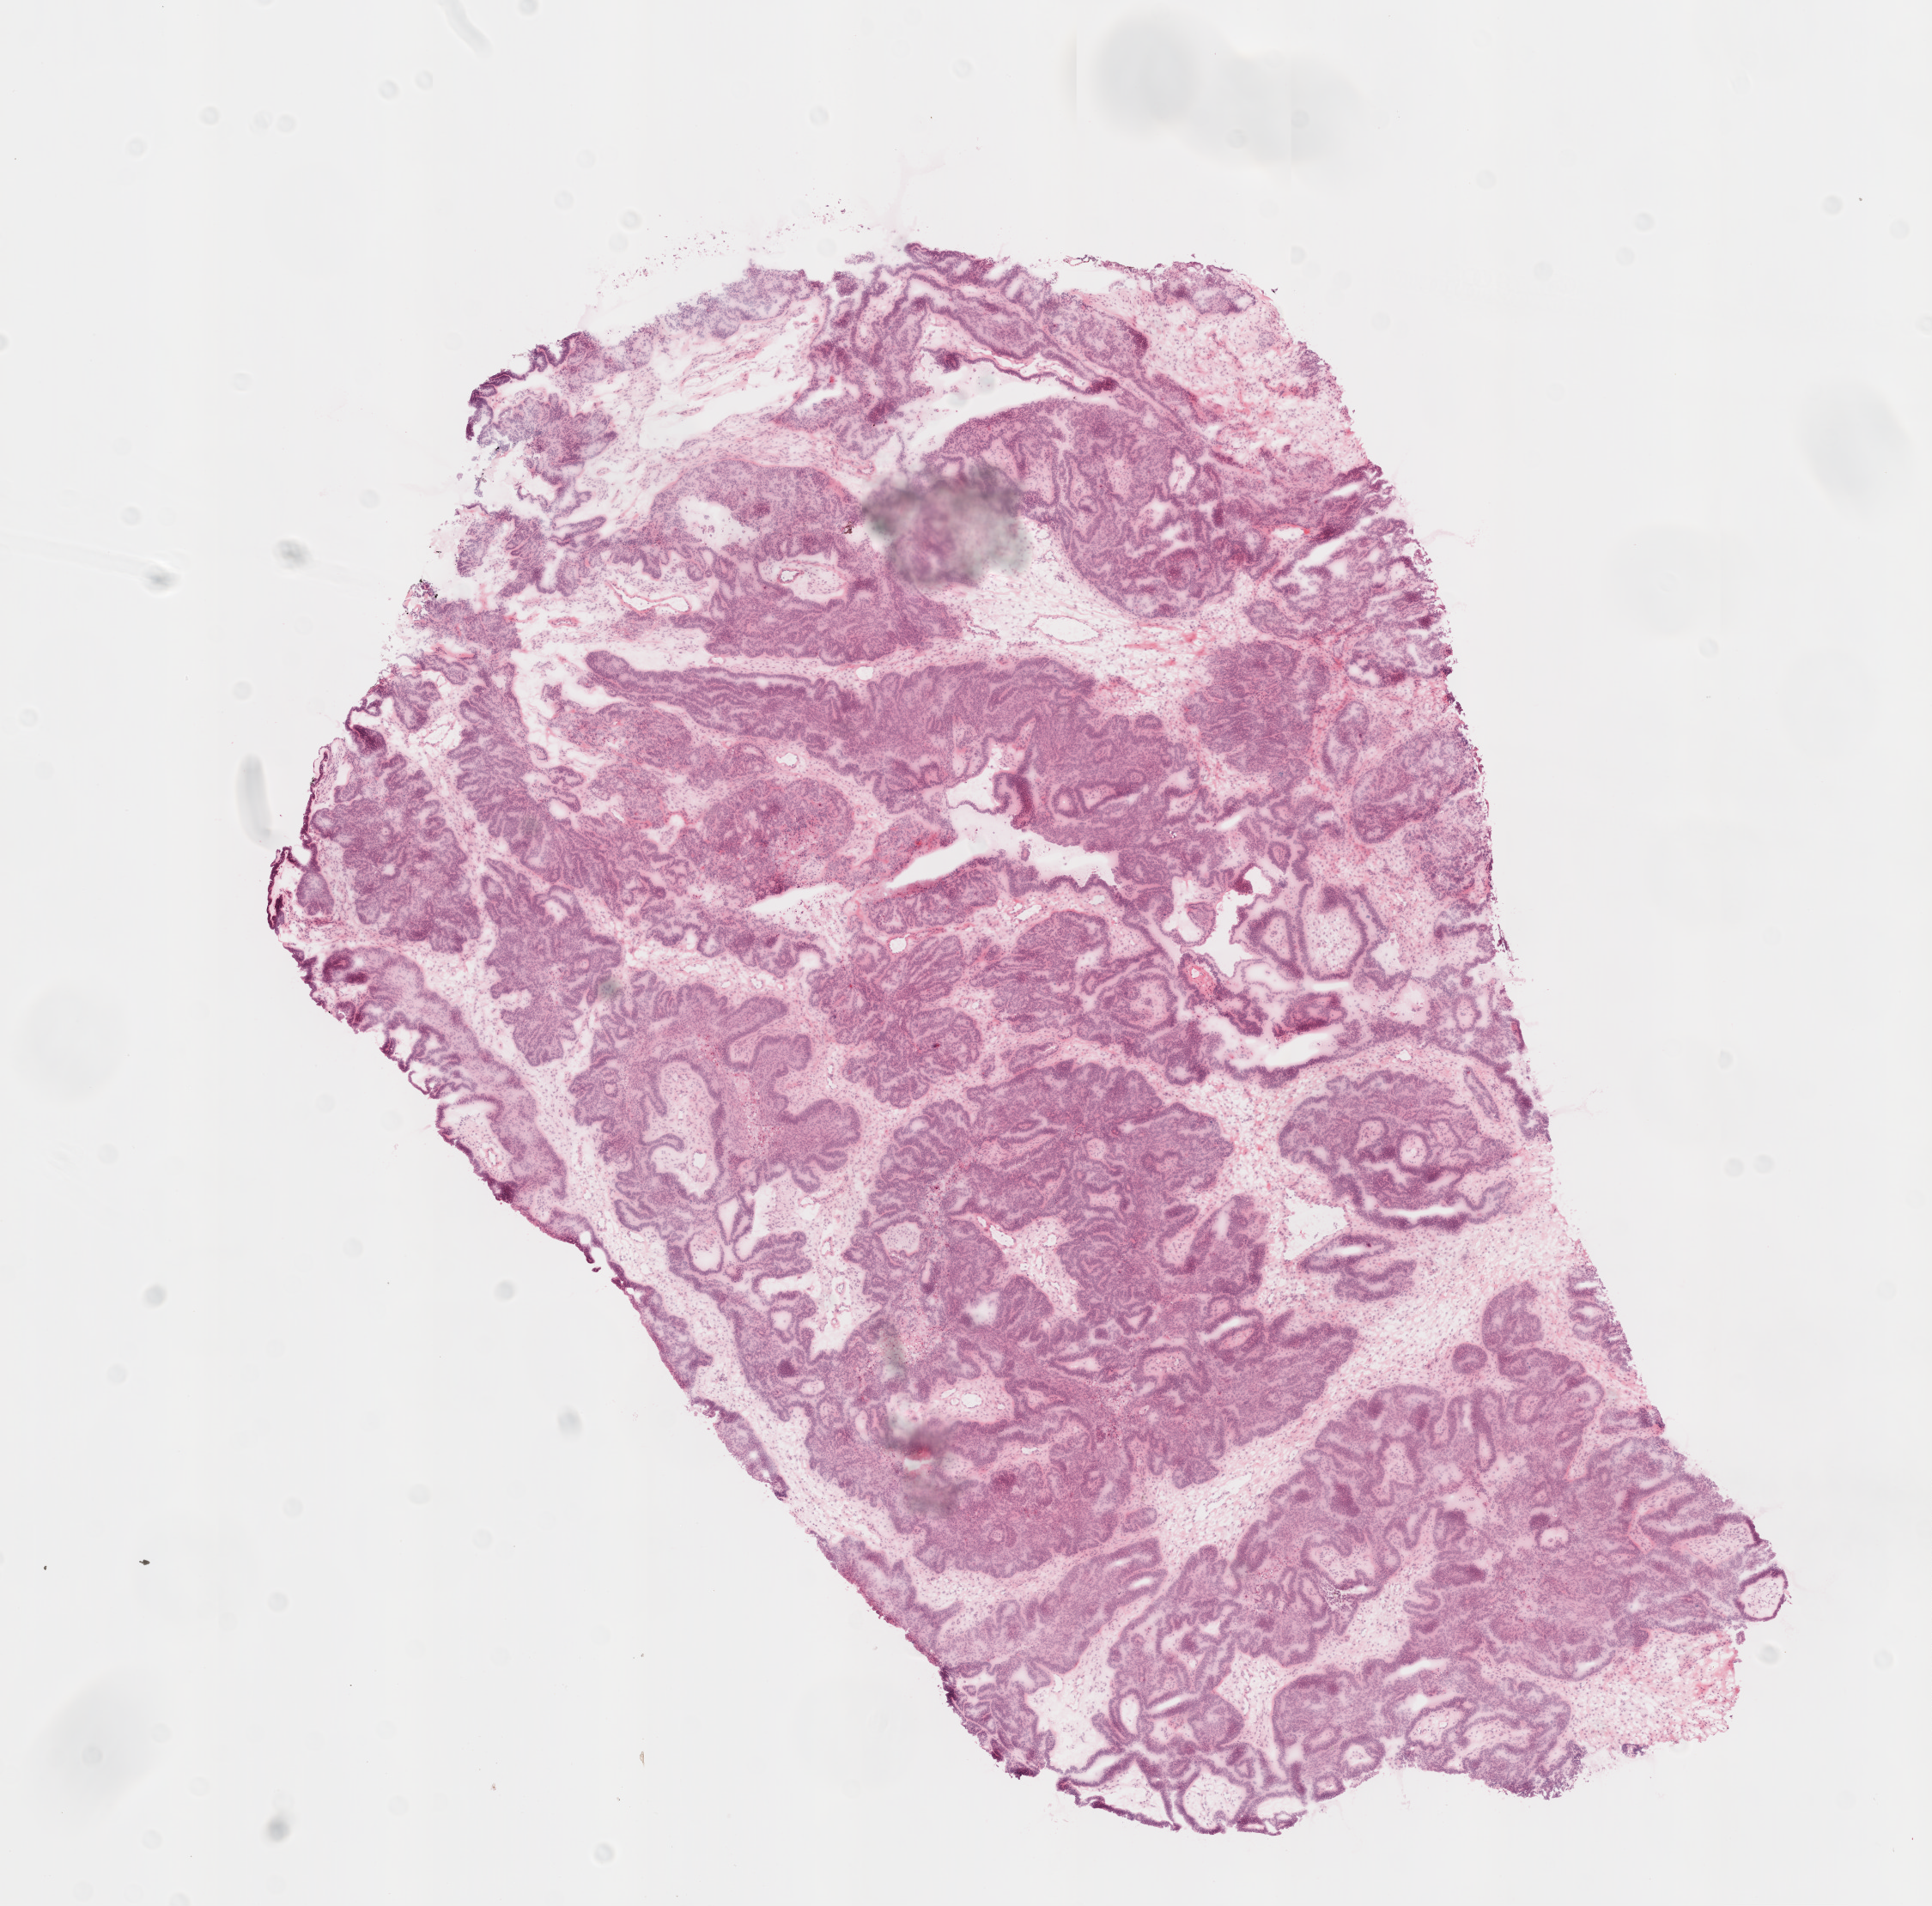
Hematoxylin and eosin (H&E) stained whole-slide image — shown as a low-resolution overview of the whole scanned area (about 9.0 x 8.9 mm, slide scanned at 20x). Frozen section from the top of the tissue portion. Ovary, primary tumour sample. Female patient; age at initial diagnosis 65 years. Histologic grade: G2 (moderately differentiated). Pathologist review of this section (percent, as recorded): tumour cells 90%, tumour nuclei 98%, normal cells 0%, stromal cells 10%, necrosis 0%.
FIGO stage: IIA. Diagnosis: Serous cystadenocarcinoma, NOS.